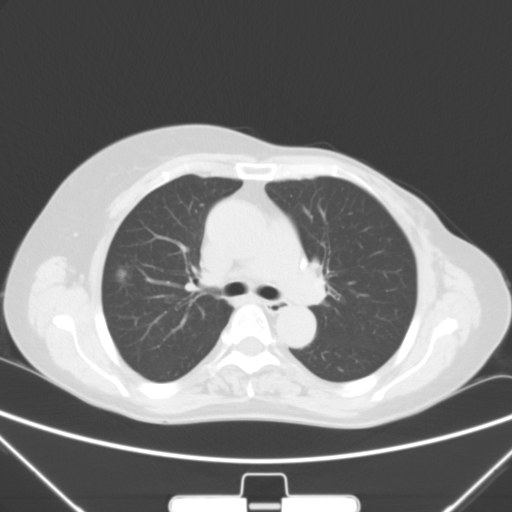
Chest CT, one axial slice; position 33 of 53 along the scan axis; 120 kVp; lung window (W 1500 / L -600 HU); 512 × 512 image matrix. Female patient, age 64 years. From the clinical record (not read from this slice): clinical TNM (as recorded): T1c N0 M0; histopathological grade: G1-2.
Structures marked on this image (rectangle marked by the reading radiologist):
- lung tumour (recorded histology: adenocarcinoma): bounding box <111,259,135,287> (left, top, right, bottom; pixels)